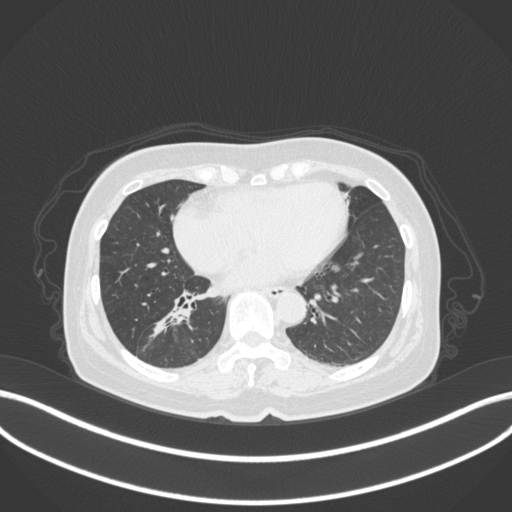
Chest CT, one axial slice; slice 154 of 429 in the series (ordered by position); 120 kVp; lung window (W 1500 / L -600 HU); 1 mm slice thickness; 512 × 512 image matrix. Patient: female, 67 years. From the clinical record (not read from this slice): clinical TNM (as recorded): T1c N1 M0; histopathological grade: G2-3.
Outlined on this slice (bounding box drawn by a radiologist):
- lung tumour (recorded histology: adenocarcinoma): bounding box [x1, y1, x2, y2] px = [147, 296, 197, 340]